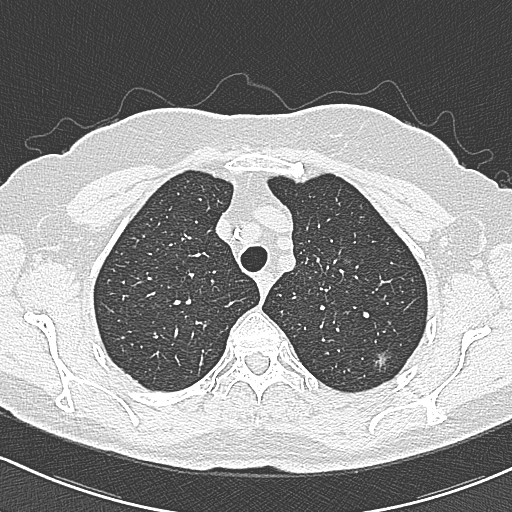
Low-dose screening chest CT, axial slice, first (baseline) screen, lung window (W 1500 / L -600 HU), 1 mm slice thickness, lung (sharp) reconstruction kernel (B80f). Female, age 65 years at enrolment.
Expert-annotated lung lesion, box from (x=368, y=345) to (x=404, y=381) px. The screening reader recorded 3 non-calcified nodules or masses ≥4 mm on this exam (left upper lobe, left upper lobe, right upper lobe); which of them this box marks is not recorded. Official screen result: positive, change unspecified: nodule(s) >= 4 mm or enlarging nodule(s), mass(es), or other non-specific abnormalities suspicious for lung cancer. Lung cancer was diagnosed 390 days after this screen (after the second annual screen): bronchiolo-alveolar carcinoma, non-mucinous, left upper lobe, stage IA (AJCC 6th edition), 10 mm at pathology.